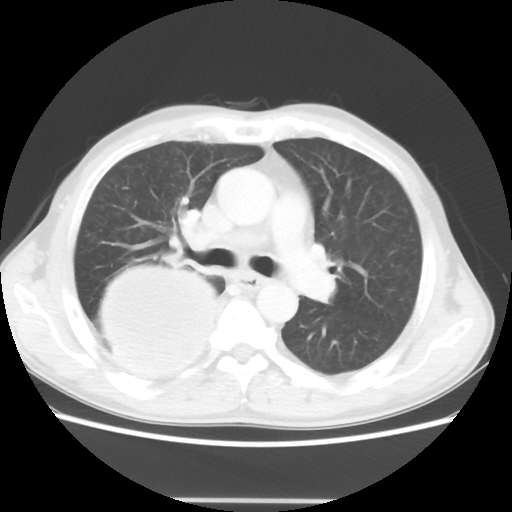
Chest CT, one axial slice. Slice 30 of 48 in the series (ordered by position). Lung window (W 1500 / L -600 HU). 5 mm slice thickness. 512 × 512 image matrix, field of view 361 × 361 mm. Patient: male, 66 years. From the clinical record (not read from this slice): clinical TNM (as recorded): T4 N1 M1; histopathological grade: G3.
Annotated regions visible in this slice (bounding box drawn by a radiologist):
- lung tumour (recorded histology: small cell carcinoma): bounding box <91,258,227,392> (left, top, right, bottom; pixels)